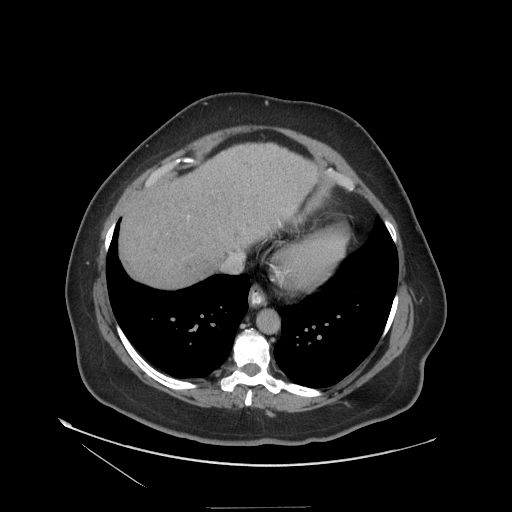
Contrast-enhanced abdominal CT (liver protocol), one axial slice; position 102 of 127 along the scan axis; reconstruction kernel STANDARD; 140 kVp; soft-tissue window (W 400 / L 40 HU); 512 × 512 image matrix. Case-level facts recorded for this patient, not image findings: diagnosis: hepatocellular carcinoma (patient treated with transarterial chemoembolisation; whether this scan precedes or follows treatment is not stated here); TNM stage (as recorded): Stage-II; Child-Pugh class: A; tumour size: 3 cm.
Outlined on this slice (semi-automatic segmentation, software-assisted and operator-edited):
- liver parenchyma outside the tumour (the mass and vessels are separate outlines, so this box may not span the whole liver): bounding box <120,144,318,286> (left, top, right, bottom; pixels)
- liver vessels: <147,181,151,185>